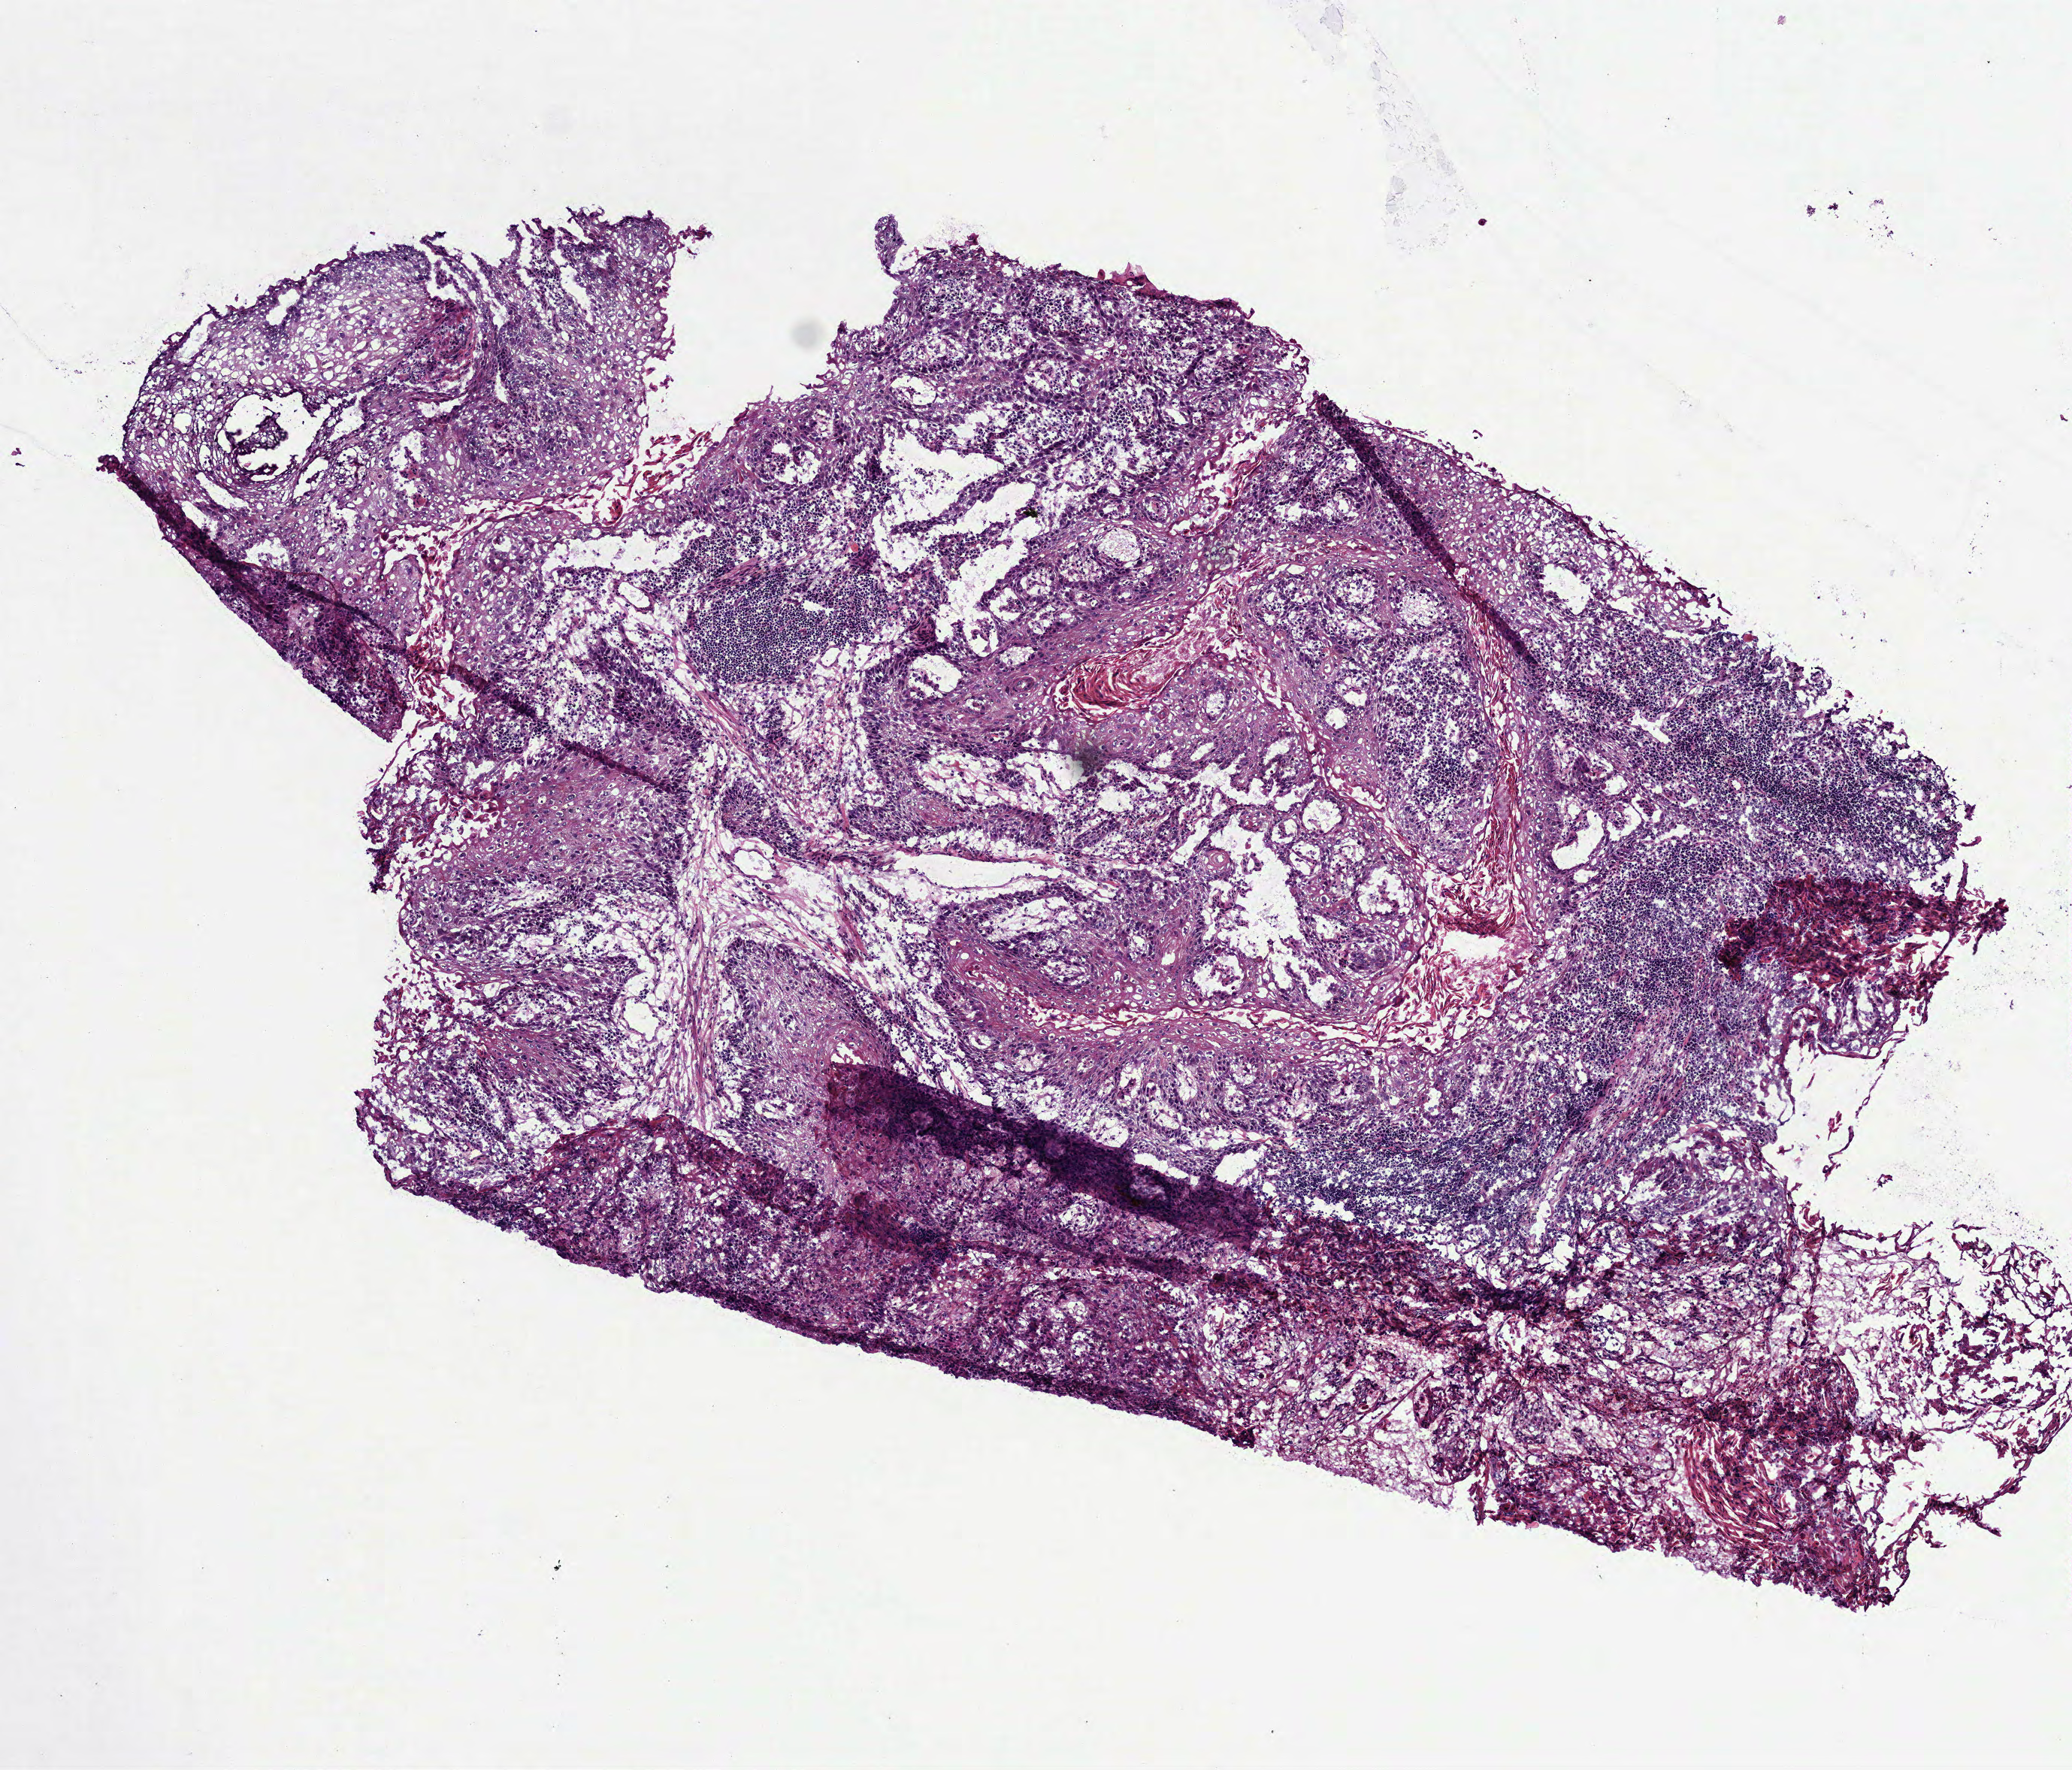
Hematoxylin and eosin (H&E) stained whole-slide image — whole scanned area (about 5.6 x 4.7 mm) shown as a low-resolution overview, frozen section from the top of the tissue portion, sample: primary tumour, head and neck. Patient: female, age at initial diagnosis 63 years. Histologic grade: G2 (moderately differentiated). Composition of this section per pathologist review: tumour cells 75%, tumour nuclei 60%, normal cells 0%, stromal cells 25%, necrosis 0%.
Pathologic diagnosis: Squamous cell carcinoma, NOS (larynx, NOS).